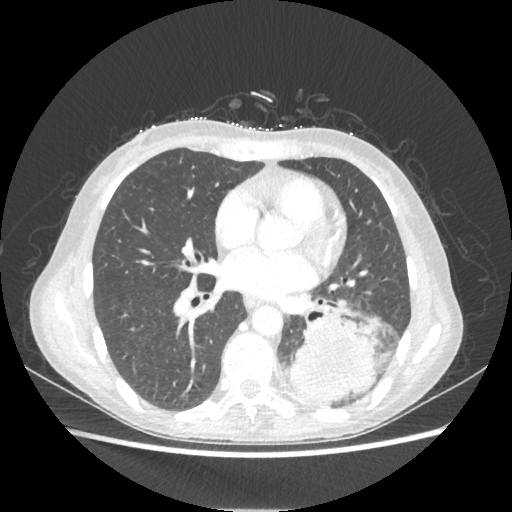
Chest CT, one axial slice. Slice 101 of 221 in the series (ordered by position). Reconstruction kernel STANDARD. 80 kVp. Lung window (W 1500 / L -600 HU). 1.25 mm slice thickness. 512 × 512 image matrix, field of view 360 × 360 mm. Patient: female, 53 years. From the clinical record (not read from this slice): clinical TNM (as recorded): T3 N0 M0.
Structures marked on this image (rectangle marked by the reading radiologist):
- lung tumour (recorded histology: adenocarcinoma): bounding box (x1, y1, x2, y2) in pixels: (284, 314, 380, 407)